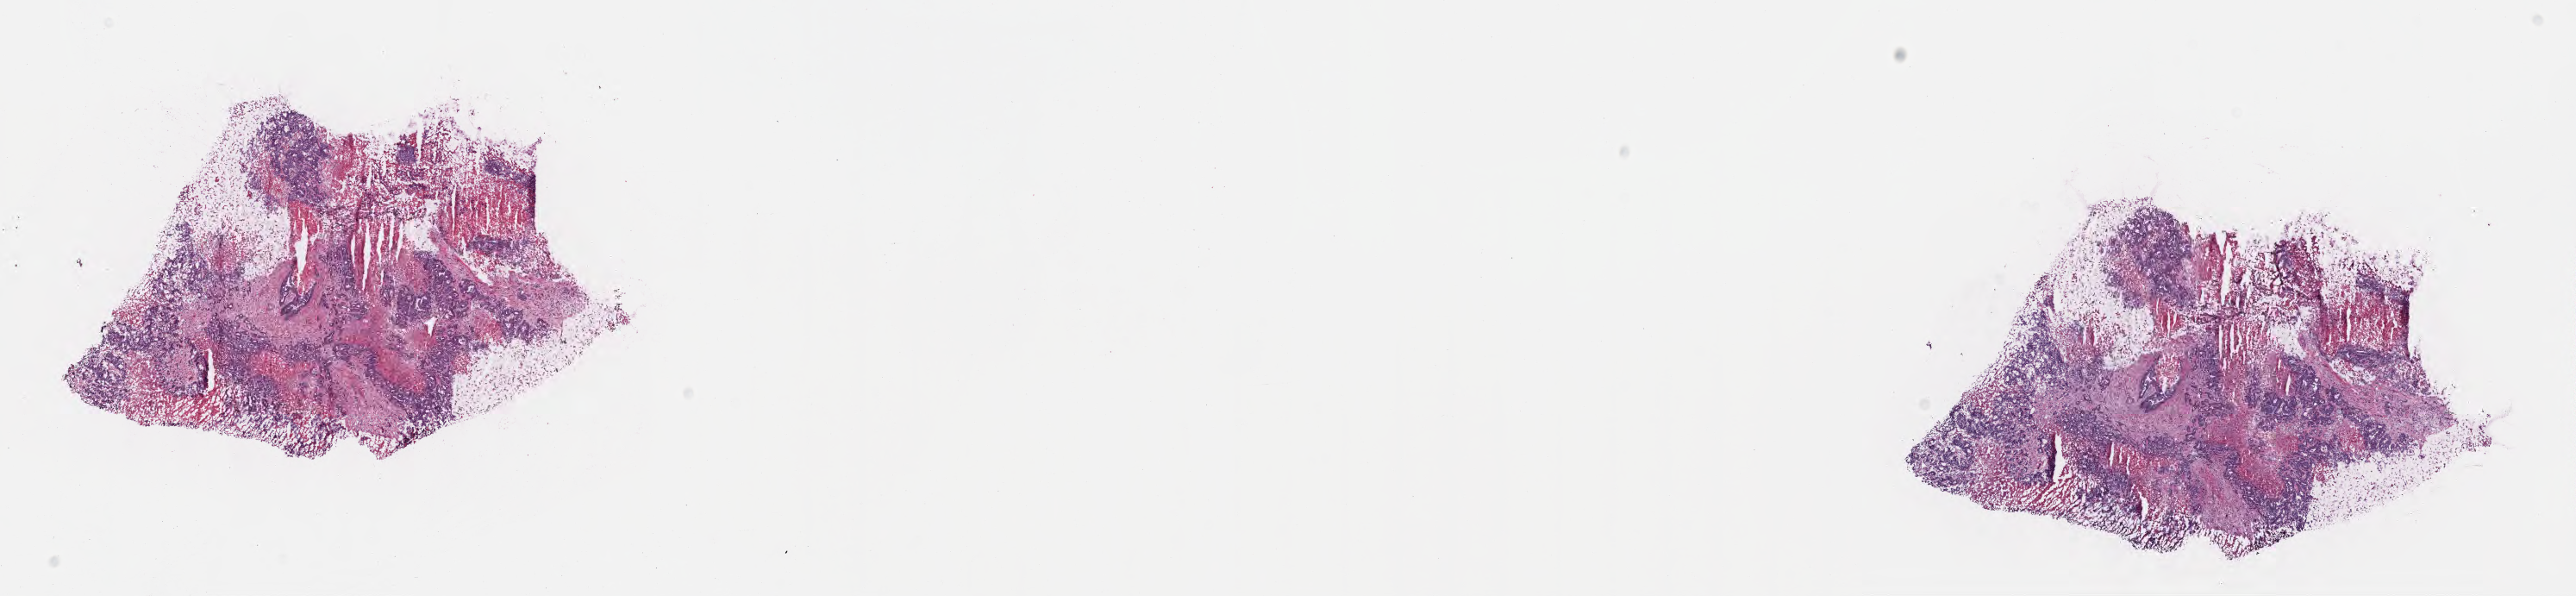
Digitized haematoxylin and eosin-stained section, a low-resolution overview of the entire scanned area, about 24.1 x 5.6 mm. Cryosection. Metastatic tumor tissue, resected from liver. Female patient; age at initial diagnosis 58 years. Slide review estimates, as recorded: tumor cells 70%, tumor nuclei 70%, stromal cells 12%, necrosis 18%, normal cells 0%. Infiltration values recorded for this section: lymphocyte infiltration 3%, monocyte infiltration 2%, neutrophil infiltration 4%.
Patient diagnosis (primary): Adenocarcinoma, NOS.